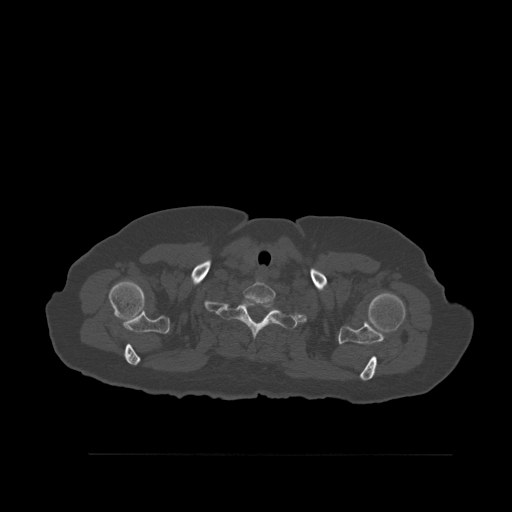
CT including the spine, one axial slice; position 446 of 527 along the scan axis; bone window (W 1800 / L 400 HU); 1.5 mm slice thickness; 512 × 512 image matrix. Female patient, age 73 years. Case-level facts recorded for this patient, not image findings: primary cancer: breast.
Annotated regions visible in this slice (semi-automatically segmented with operator editing):
- T1 vertebra: bounding box <218,299,298,358> (left, top, right, bottom; pixels)